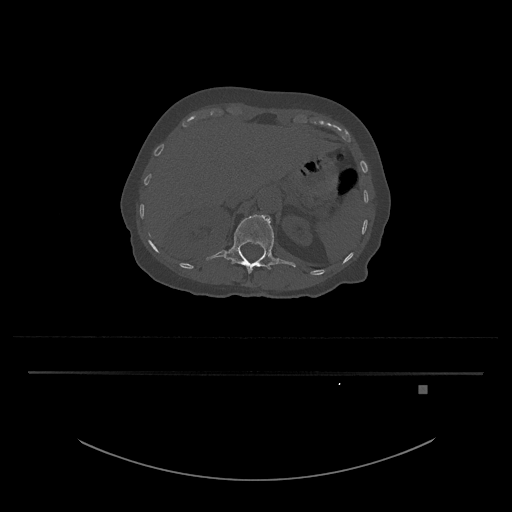
CT including the spine, one axial slice. Slice 555 of 797 in the series (ordered by position). Bone window (W 1800 / L 400 HU). 0.5 mm slice thickness. 512 × 512 image matrix, field of view 500 × 500 mm. Patient: female, 57 years. Case-level facts recorded for this patient, not image findings: primary cancer: cervical.
Annotated regions visible in this slice (semi-automatically segmented with operator editing):
- L1 vertebra: bounding box [x1, y1, x2, y2] px = [206, 214, 296, 274]